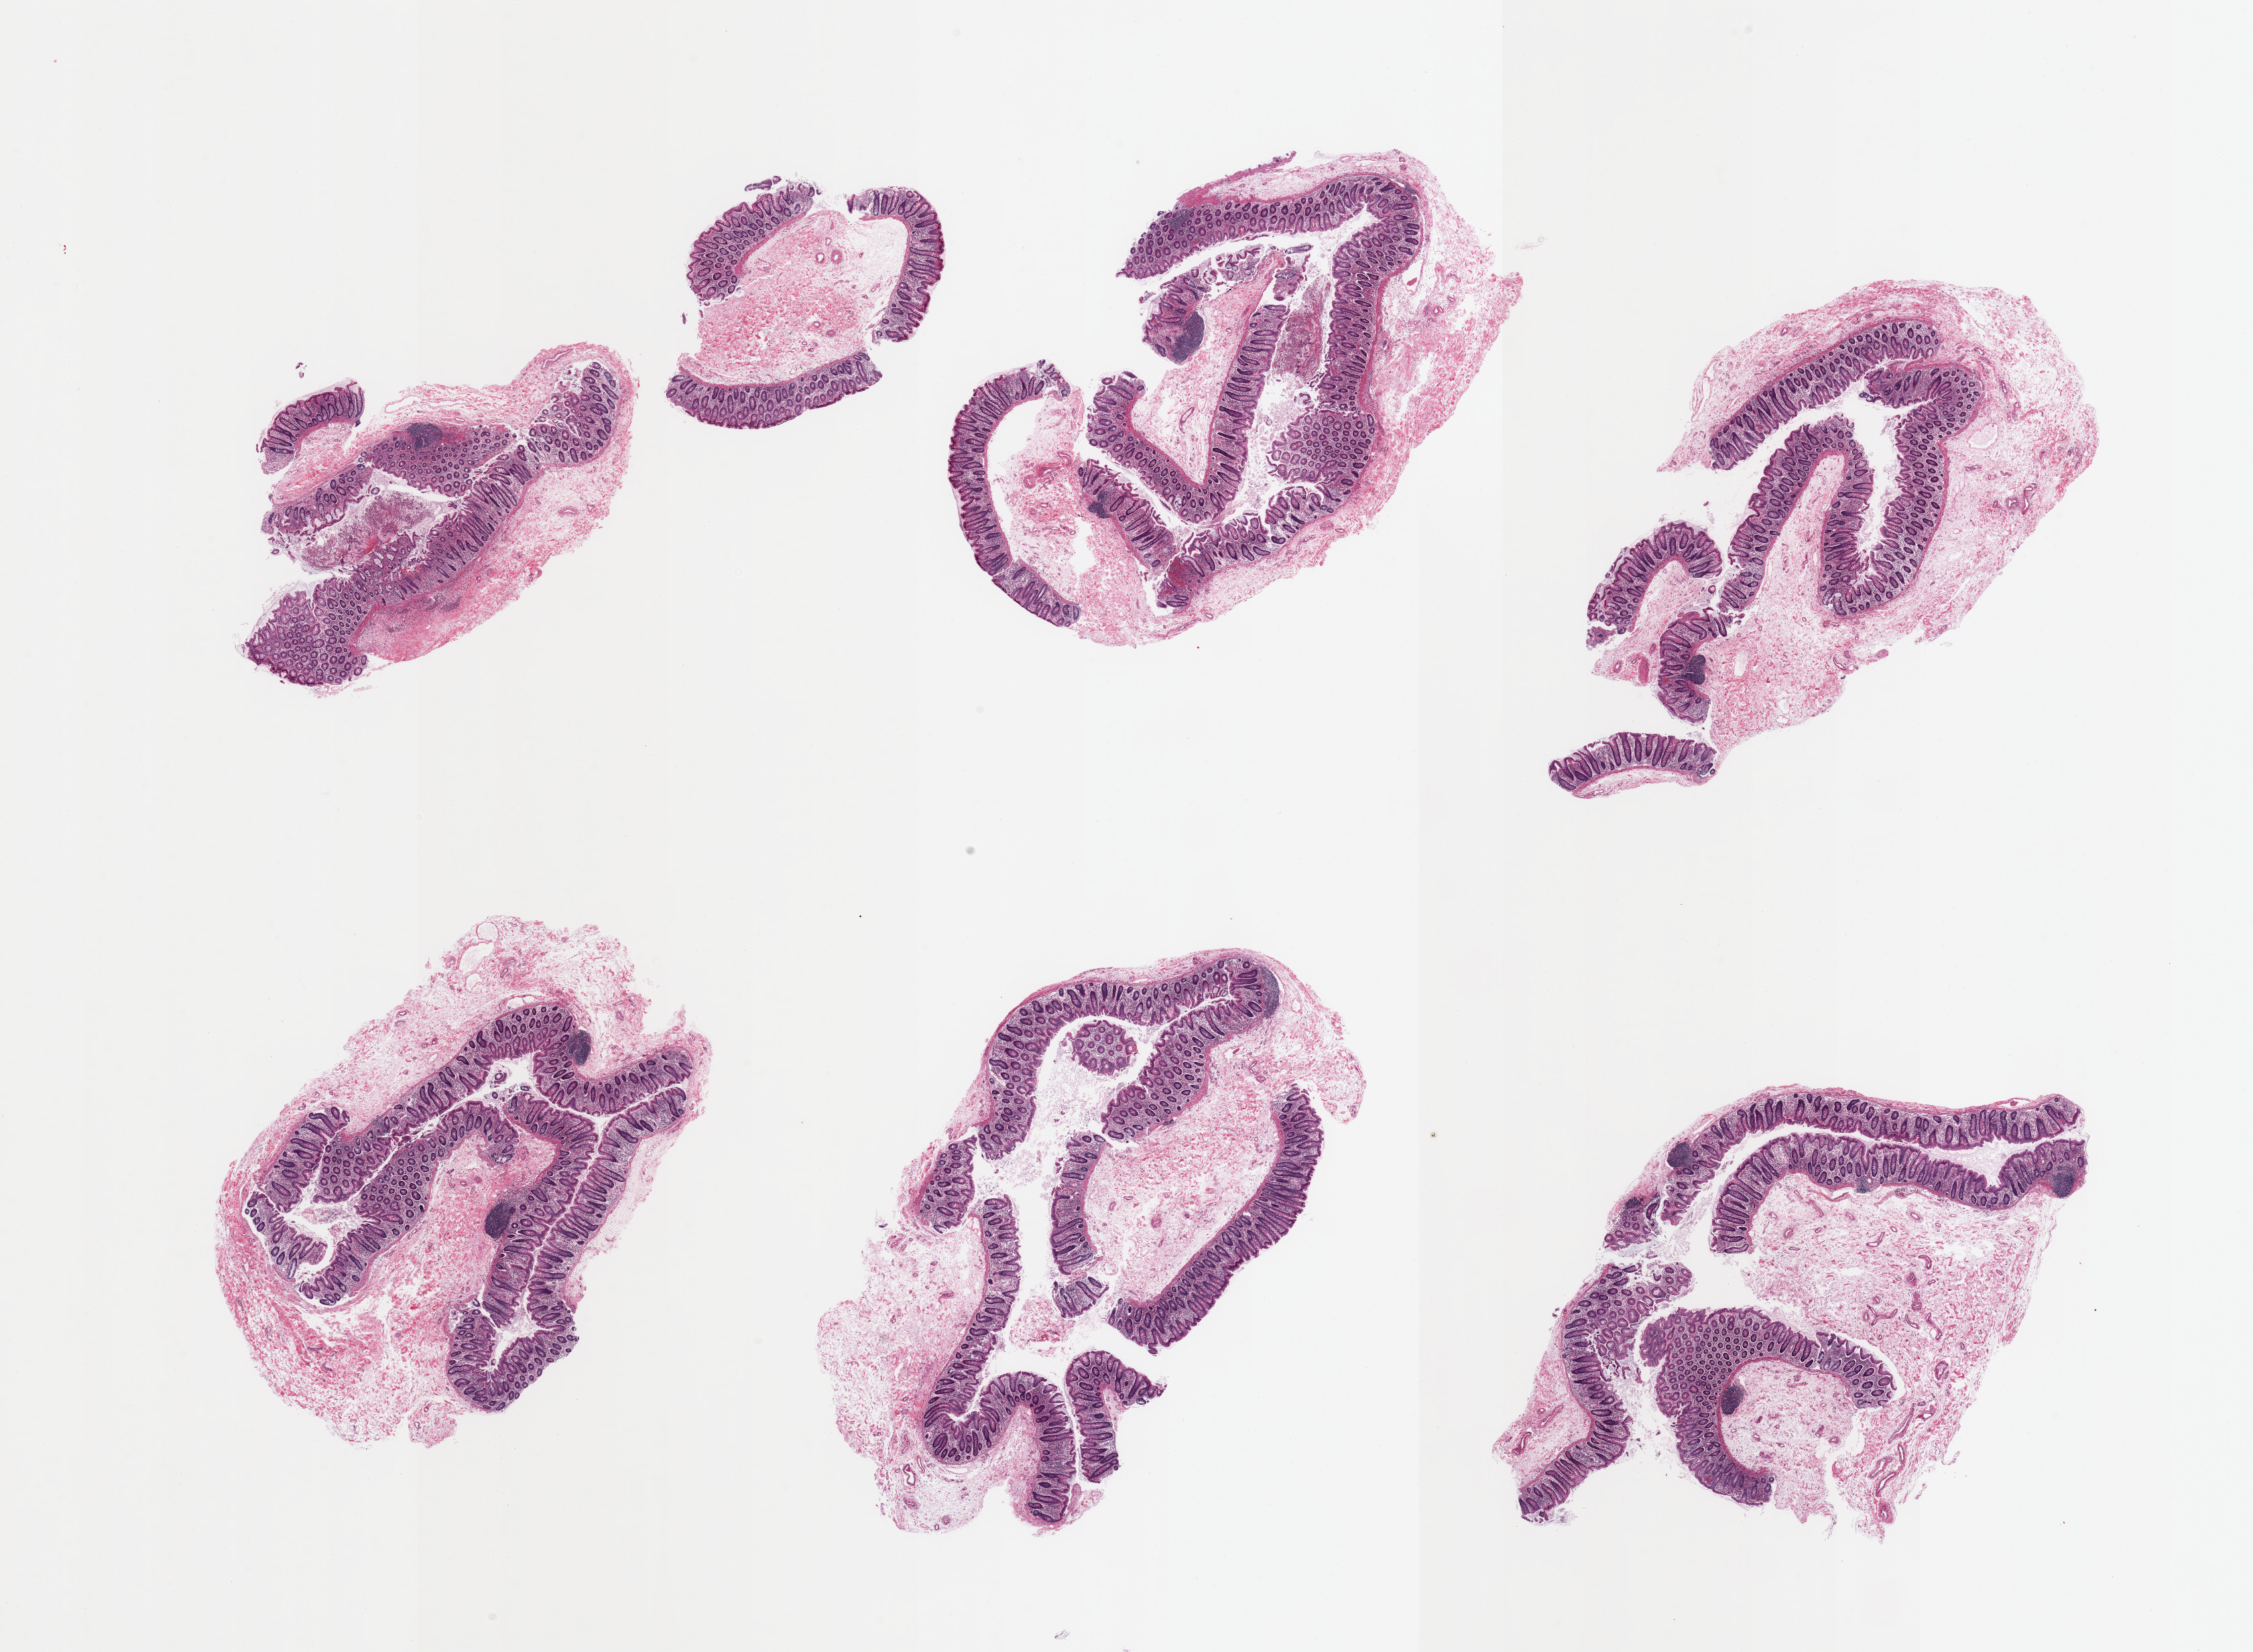
Whole-slide image, hematoxylin and eosin (H&E) stain, shown as a low-resolution overview of the whole scanned area (about 26.6 x 19.5 mm, from a 20x scan), PAXgene-fixed, paraffin-embedded tissue, sampled site (target tissue): ileum, tissue donor sample.
Pathologist's review note for this sample: 6 pieces, colon, not terminal ileum.